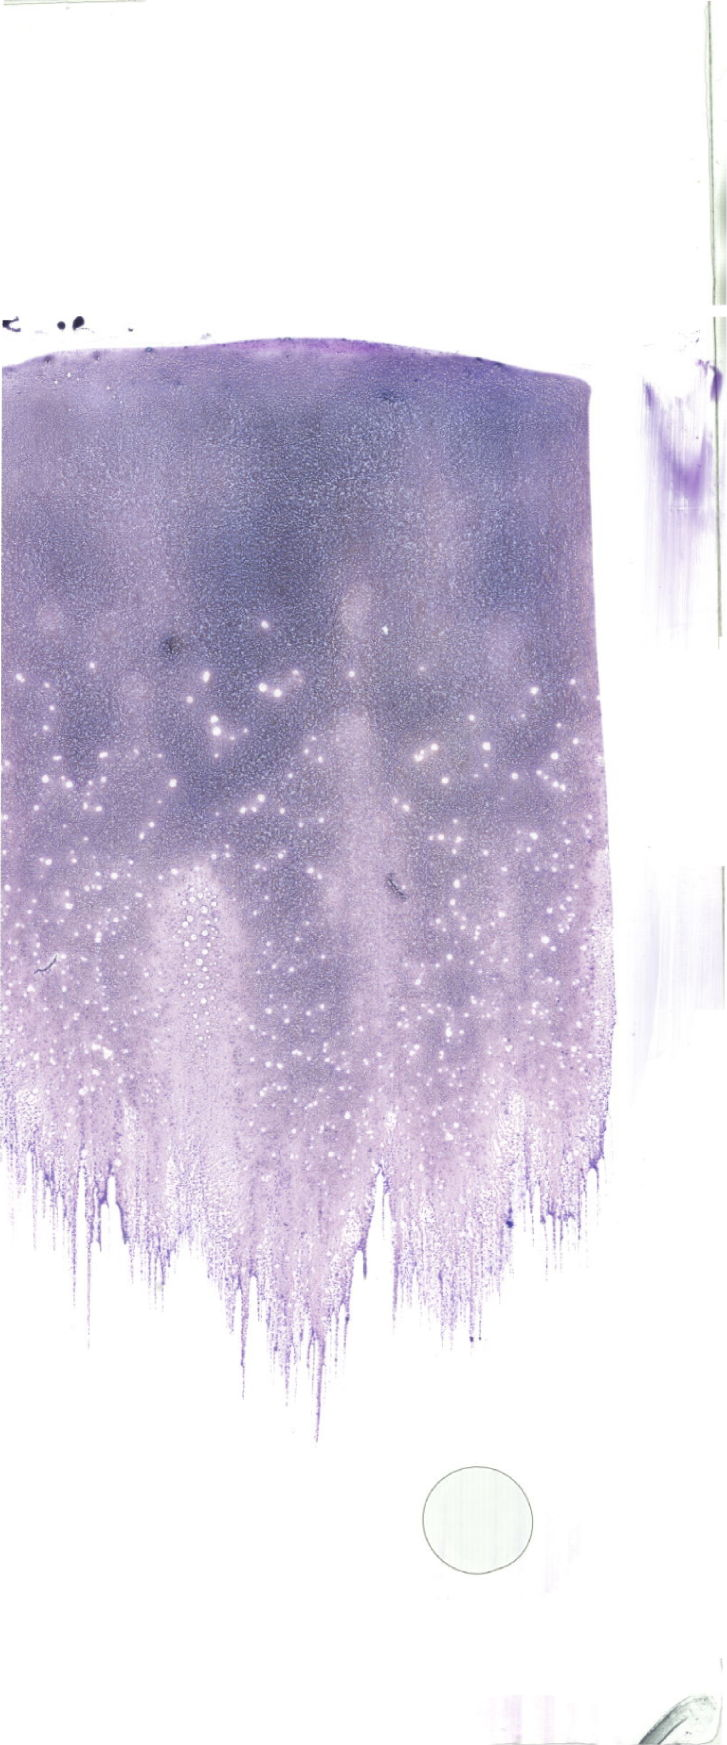
Whole-slide image of a May-Grünwald-Giemsa (MGG)-stained bone marrow aspirate smear — whole scanned area (about 20.6 x 49.5 mm) shown as a low-resolution overview. Patient sex: female.
Diagnosis: Acute Megakaryoblastic Leukemia.